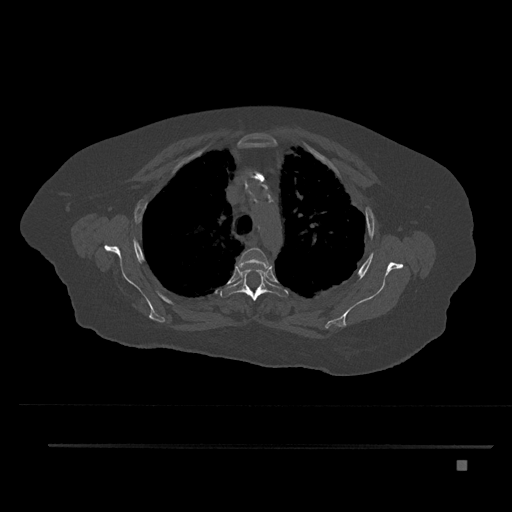
CT including the spine, one axial slice. Slice 612 of 797 in the series (ordered by position). Bone window (W 1800 / L 400 HU). 512 × 512 image matrix, field of view 437 × 437 mm. Patient: female, 76 years. From the clinical record (not read from this slice): primary cancer: lung; vertebrae with lytic lesions (as recorded): T11, L3.
Structures marked on this image (semi-automatic segmentation, software-assisted and operator-edited):
- T3 vertebra: bounding box <238,247,270,269> (left, top, right, bottom; pixels)
- T4 vertebra: <220,262,289,301>